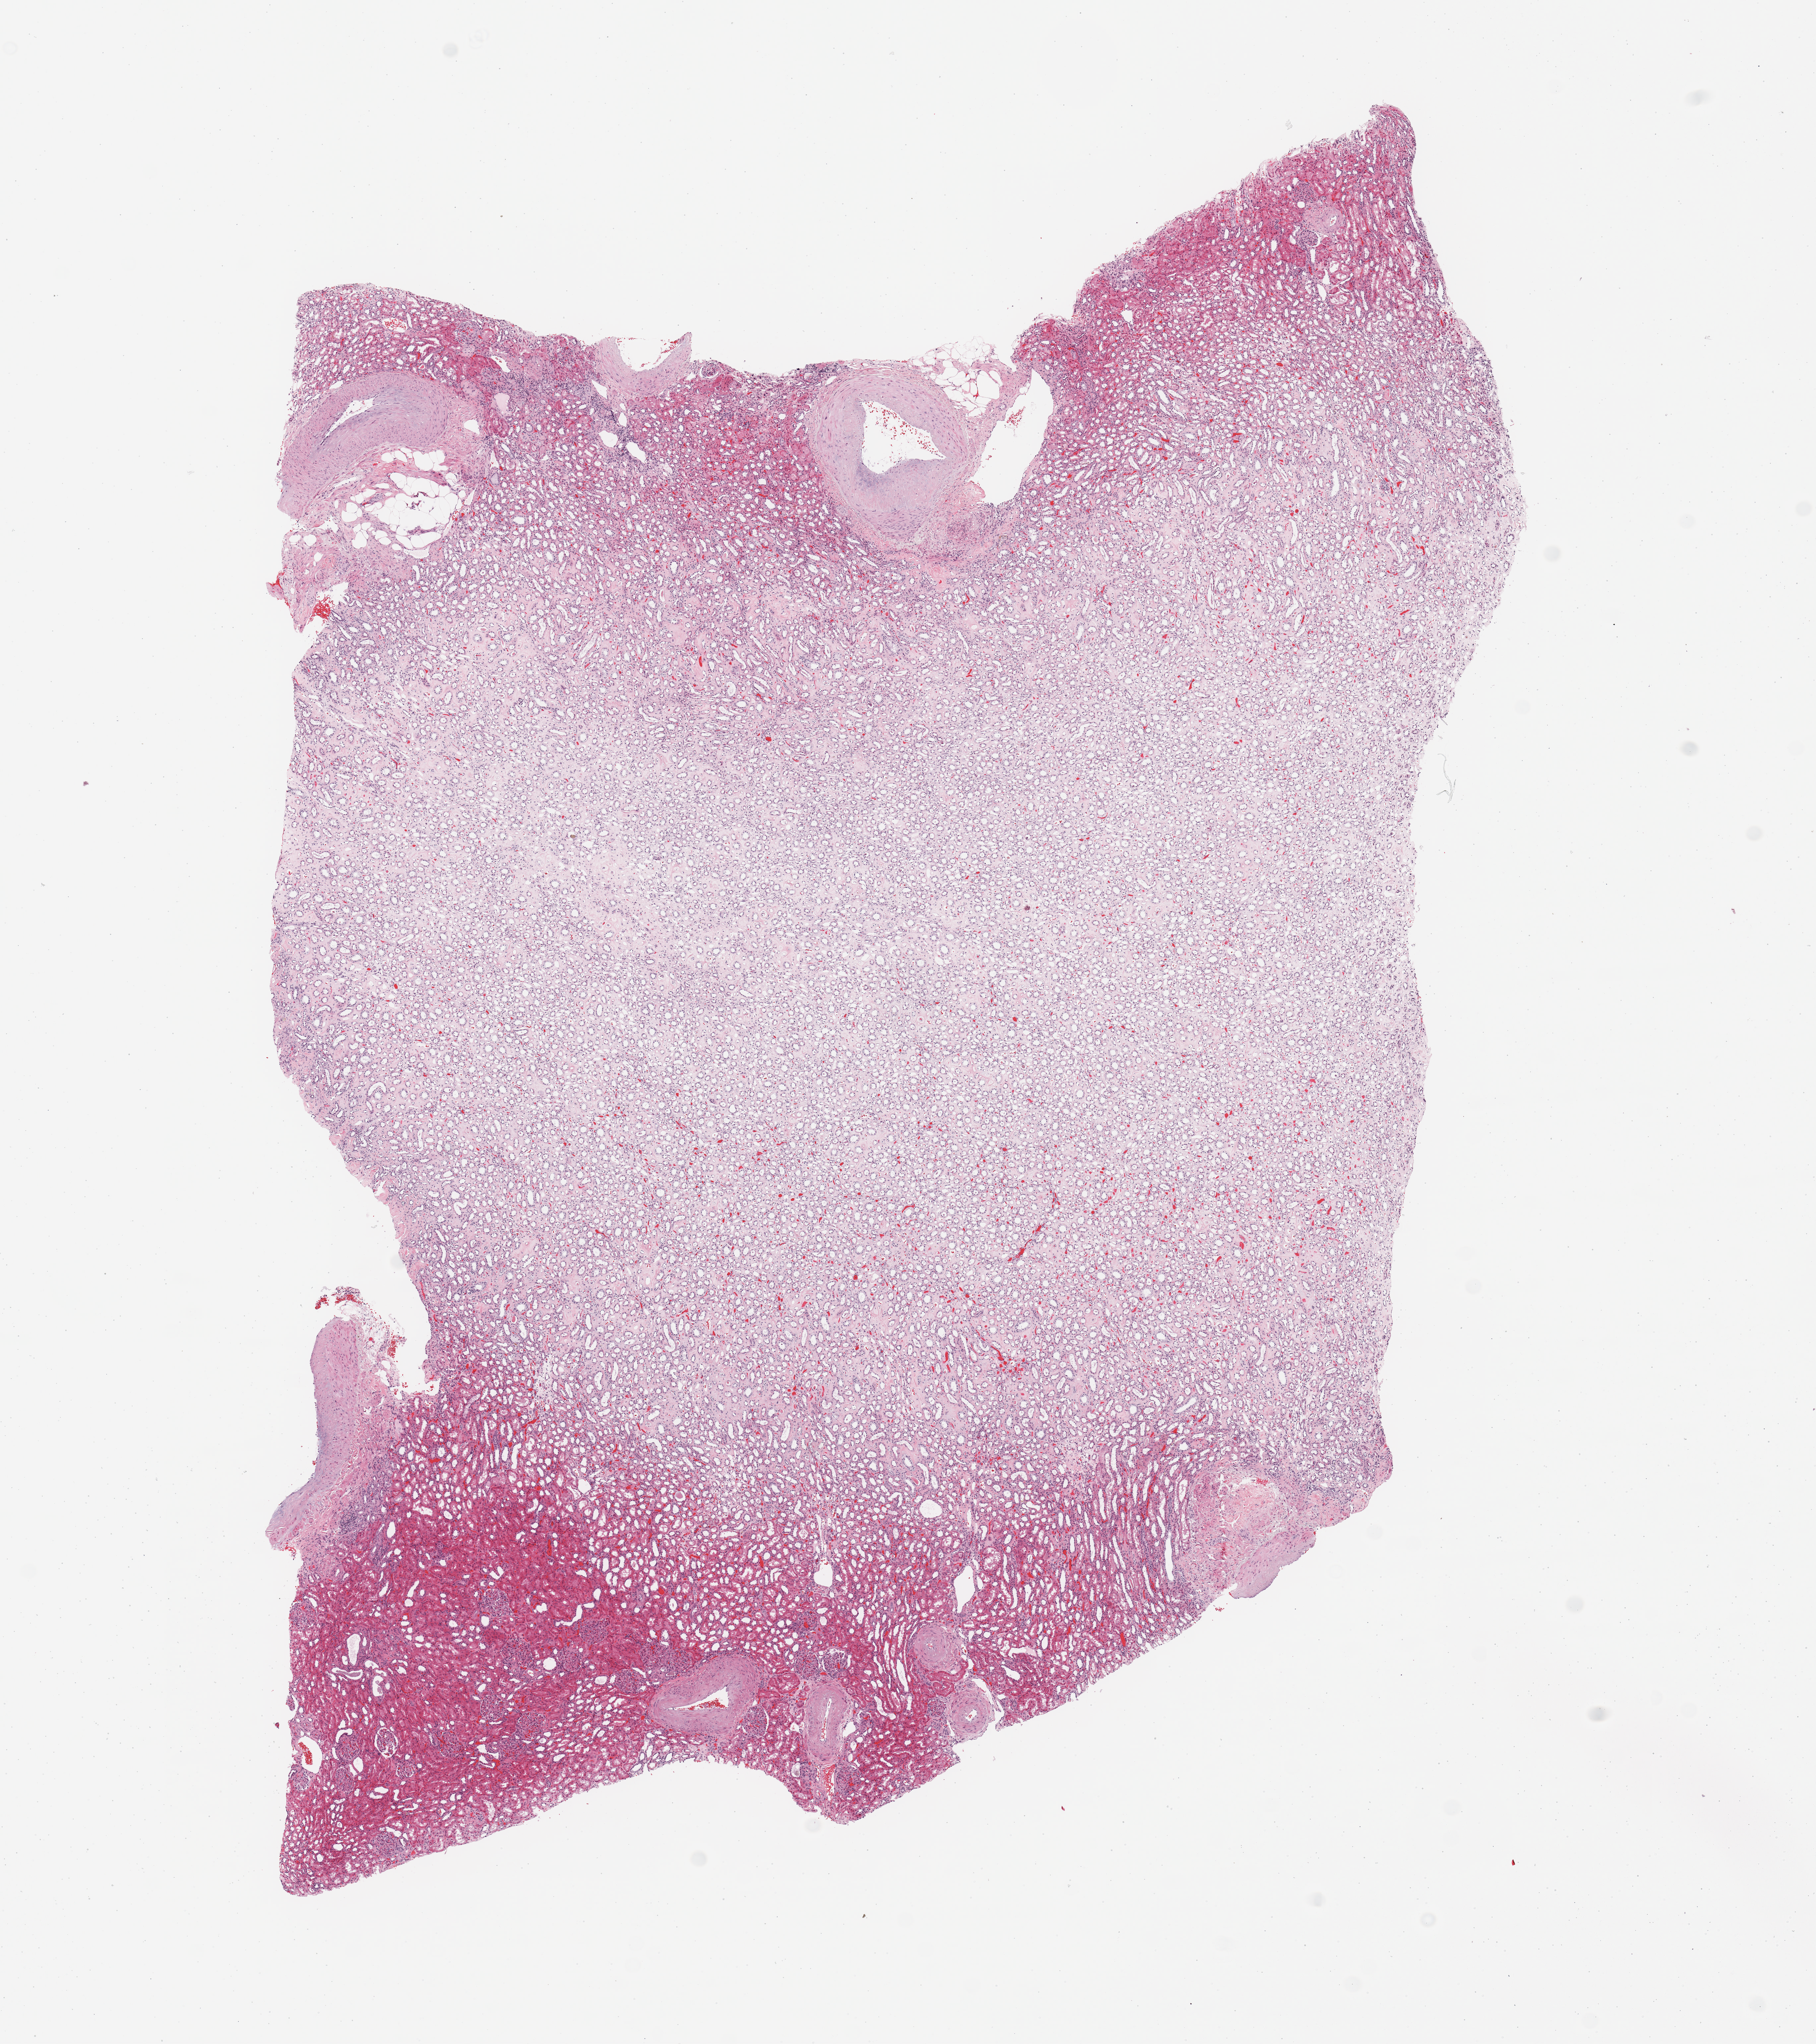
Whole-slide histology image, H&E-stained — low-resolution overview of the scanned area, about 10.8 x 12.2 mm (slide scanned at 20x), normal (non-tumour) tissue sample, sampled site: kidney. Male, 72 y/o.
* this section: normal (non-tumour) tissue from the same patient
* patient diagnosis: Renal cell carcinoma, NOS